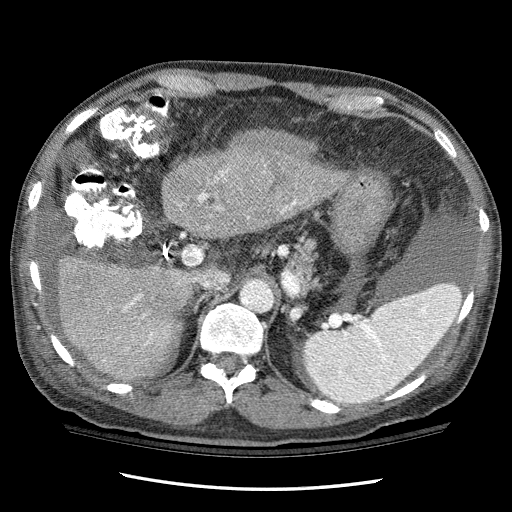
Contrast-enhanced abdominal CT (liver protocol), one axial slice. Position 68 of 114 along the scan axis. Reconstruction kernel STANDARD. One of 3 acquisitions stored at this slice position. Soft-tissue window (W 400 / L 40 HU). 2.5 mm slice thickness. 512 × 512 image matrix, field of view 360 × 360 mm. Case-level facts recorded for this patient, not image findings: diagnosis: hepatocellular carcinoma (patient treated with transarterial chemoembolisation; whether this scan precedes or follows treatment is not stated here); TNM stage (as recorded): Stage-I.
Annotated regions visible in this slice (semi-automatically segmented with operator editing):
- liver parenchyma outside the tumour (the mass and vessels are separate outlines, so this box may not span the whole liver): box from (x=52, y=143) to (x=352, y=380) px
- mass: (x=217, y=128)–(x=319, y=197)
- liver vessels: (x=124, y=177)–(x=296, y=345)